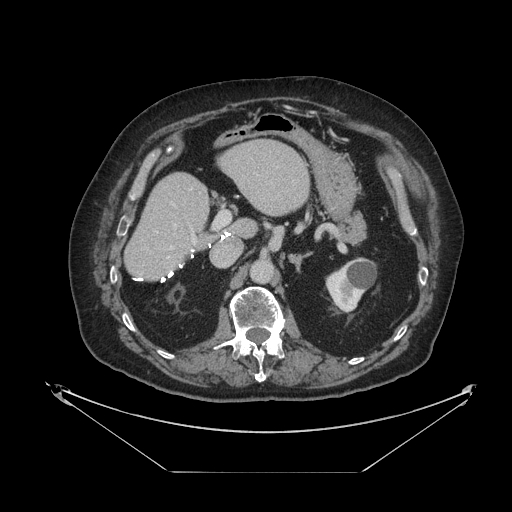
Contrast-enhanced abdominal CT, one axial slice; position 53 of 121 along the scan axis; reconstruction kernel STANDARD; intravenous contrast given; soft-tissue window (W 400 / L 40 HU); 2.5 mm slice thickness; 512 × 512 image matrix, field of view 500 × 500 mm. Male patient, age 68 years. Case-level facts recorded for this patient, not image findings: diagnosis: colorectal cancer liver metastases, imaged before liver resection.
Annotated regions visible in this slice (outlined manually by an expert reader):
- hepatic veins: bounding box [x1, y1, x2, y2] px = [168, 225, 176, 258]
- liver: [126, 141, 309, 280]
- planned liver remnant (the part of the liver to remain after resection): [126, 141, 309, 280]
- portal vein (with intrahepatic branches): [168, 204, 231, 249]